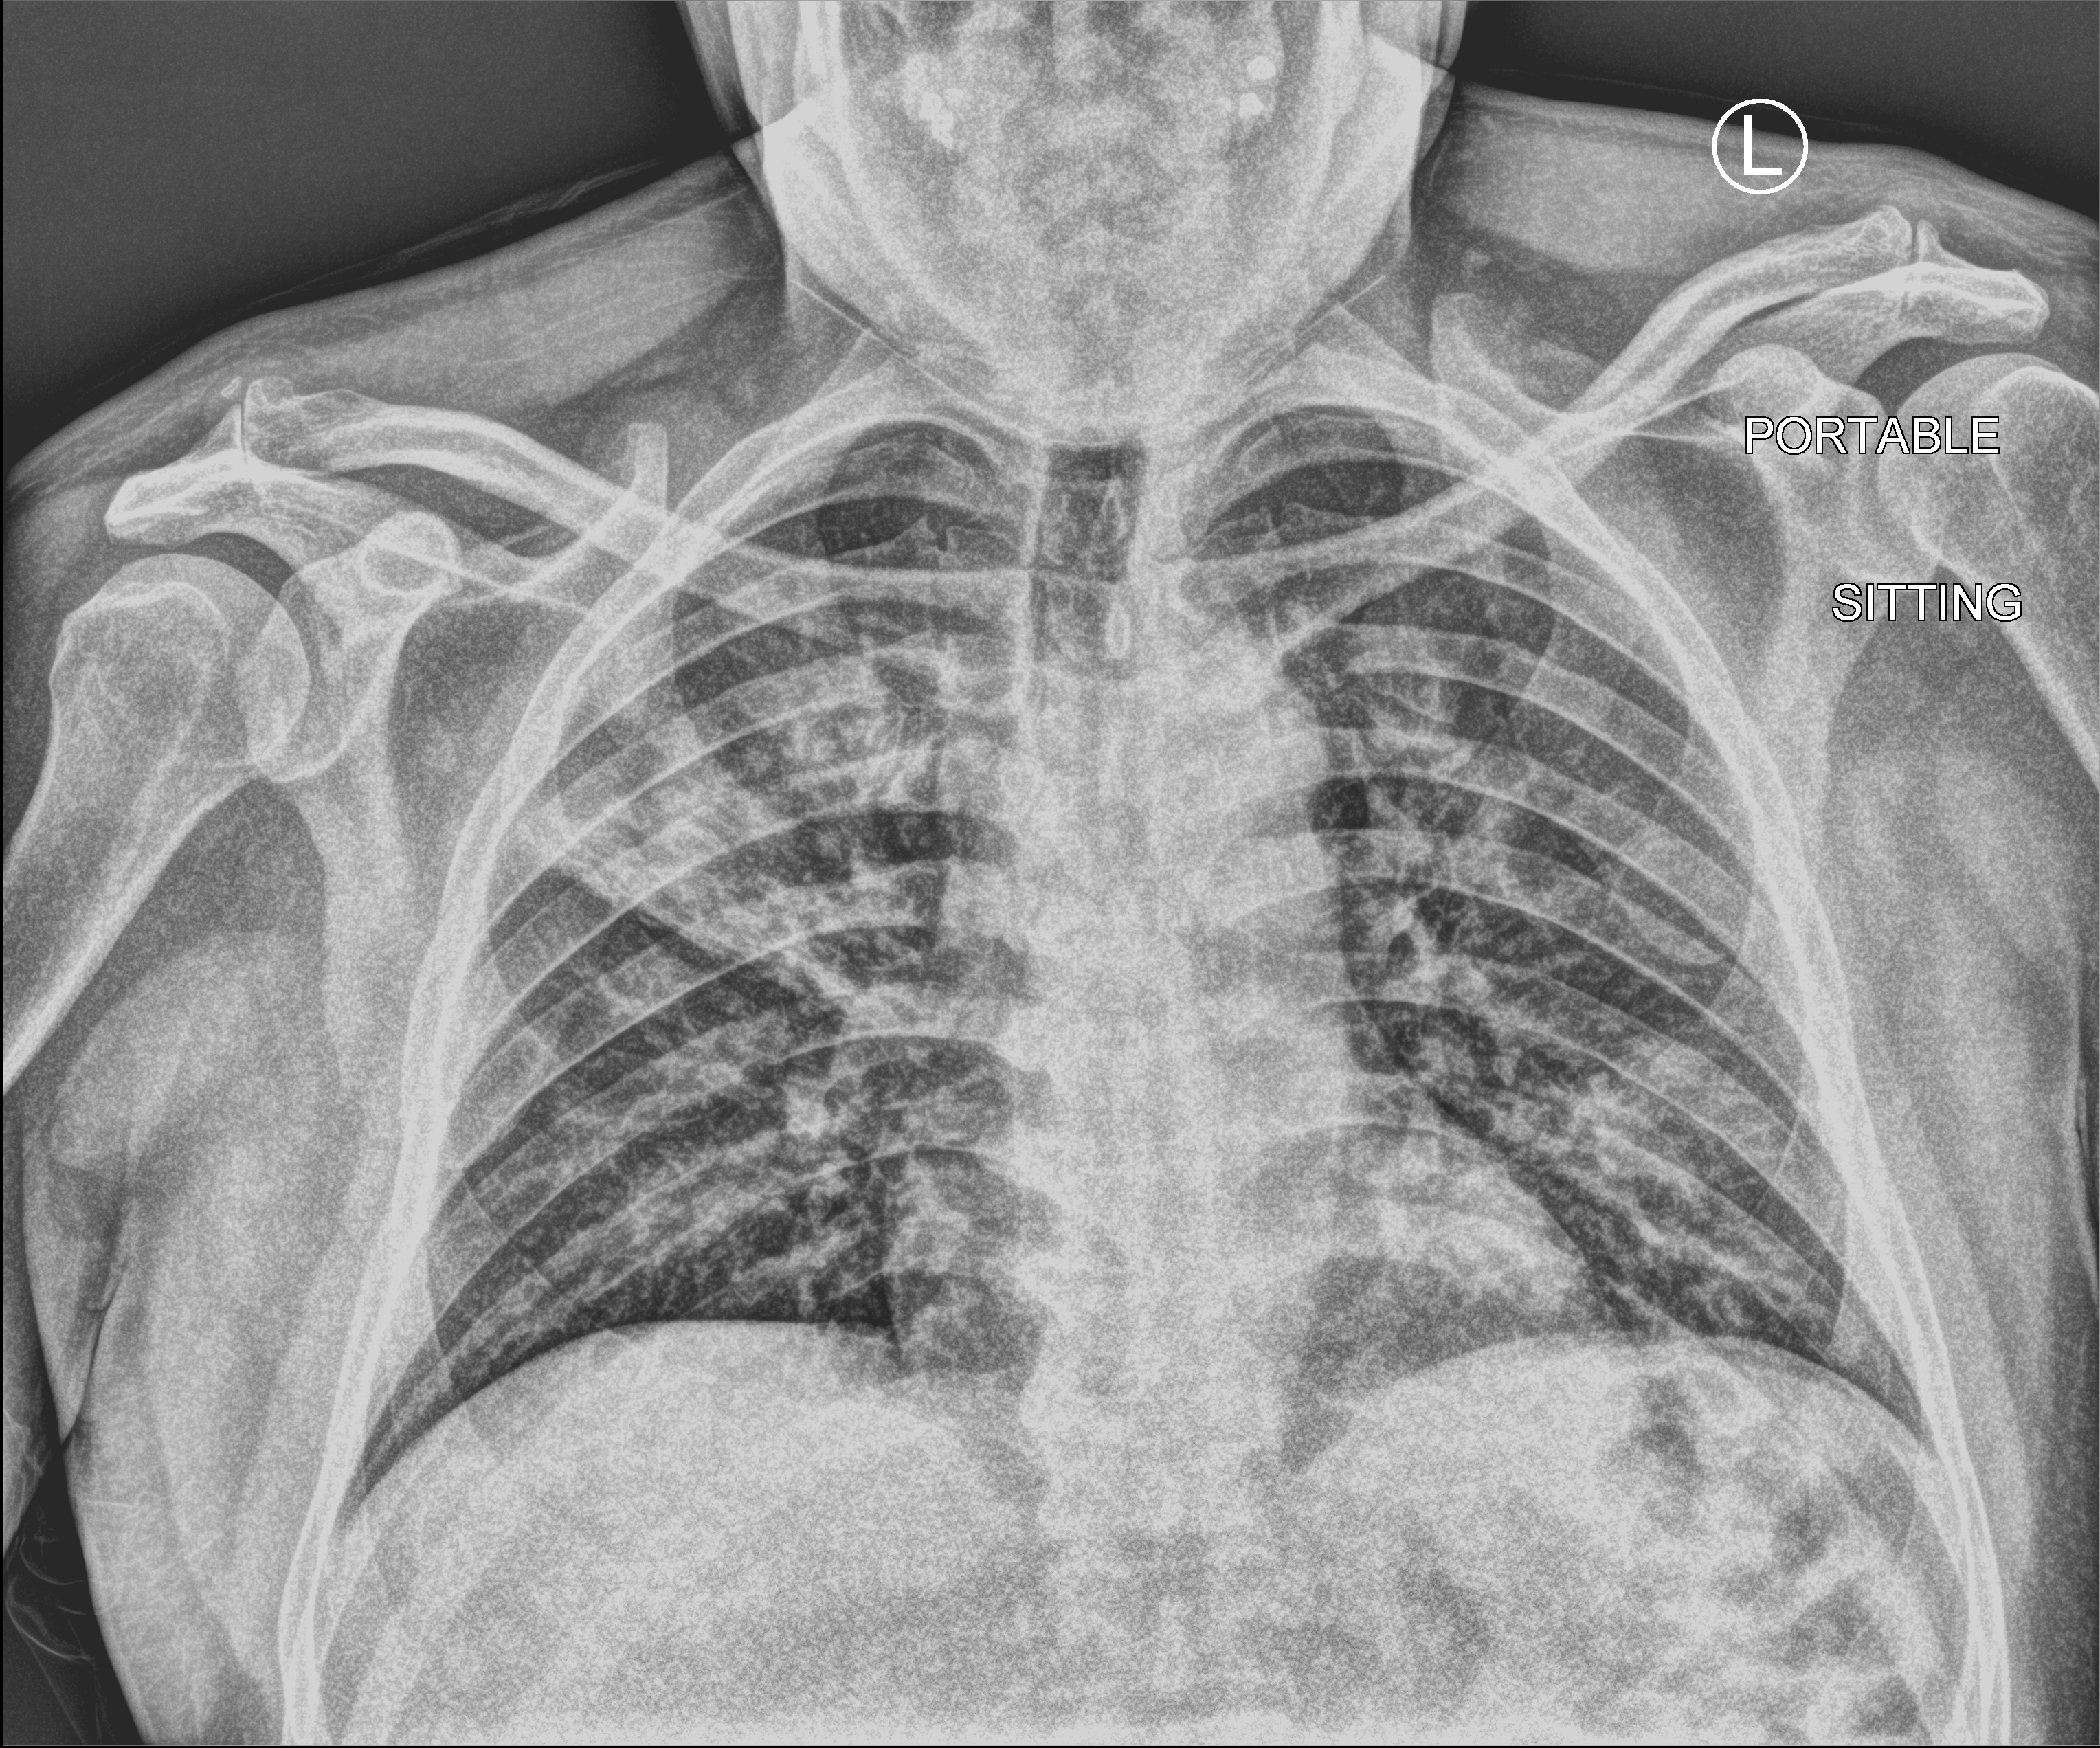
Bedside chest radiograph (computed radiography). Patient hospitalised with COVID-19; male, aged 18–59 years.
Admission-level facts for this patient (not findings on this image; timing relative to this image not recorded):
- mechanically ventilated during this hospital stay: no
- chronic kidney disease (admission record): no